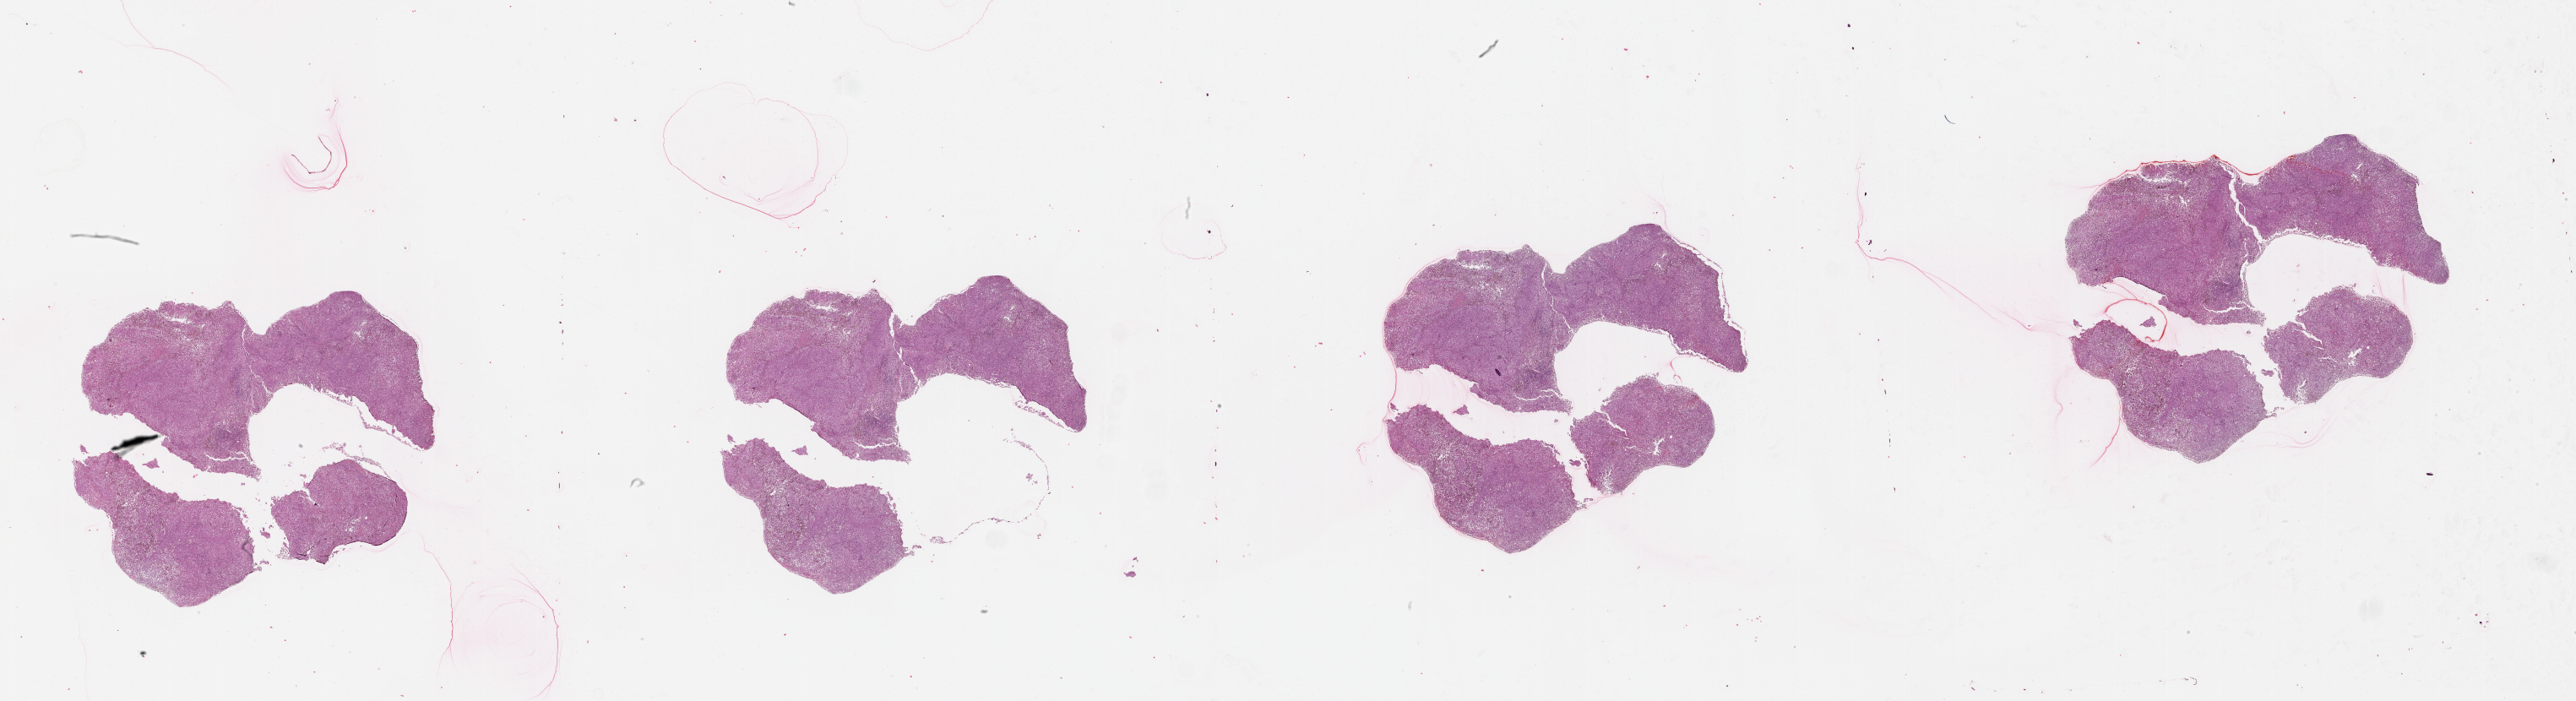
Digitized Hematoxylin and eosin (H&E) stained tissue section (whole slide), whole scanned area (about 49.1 x 13.4 mm, from a 20x scan) shown as a low-resolution overview. Male, 87 y/o.
Patient diagnosis: Malignant melanoma, NOS.